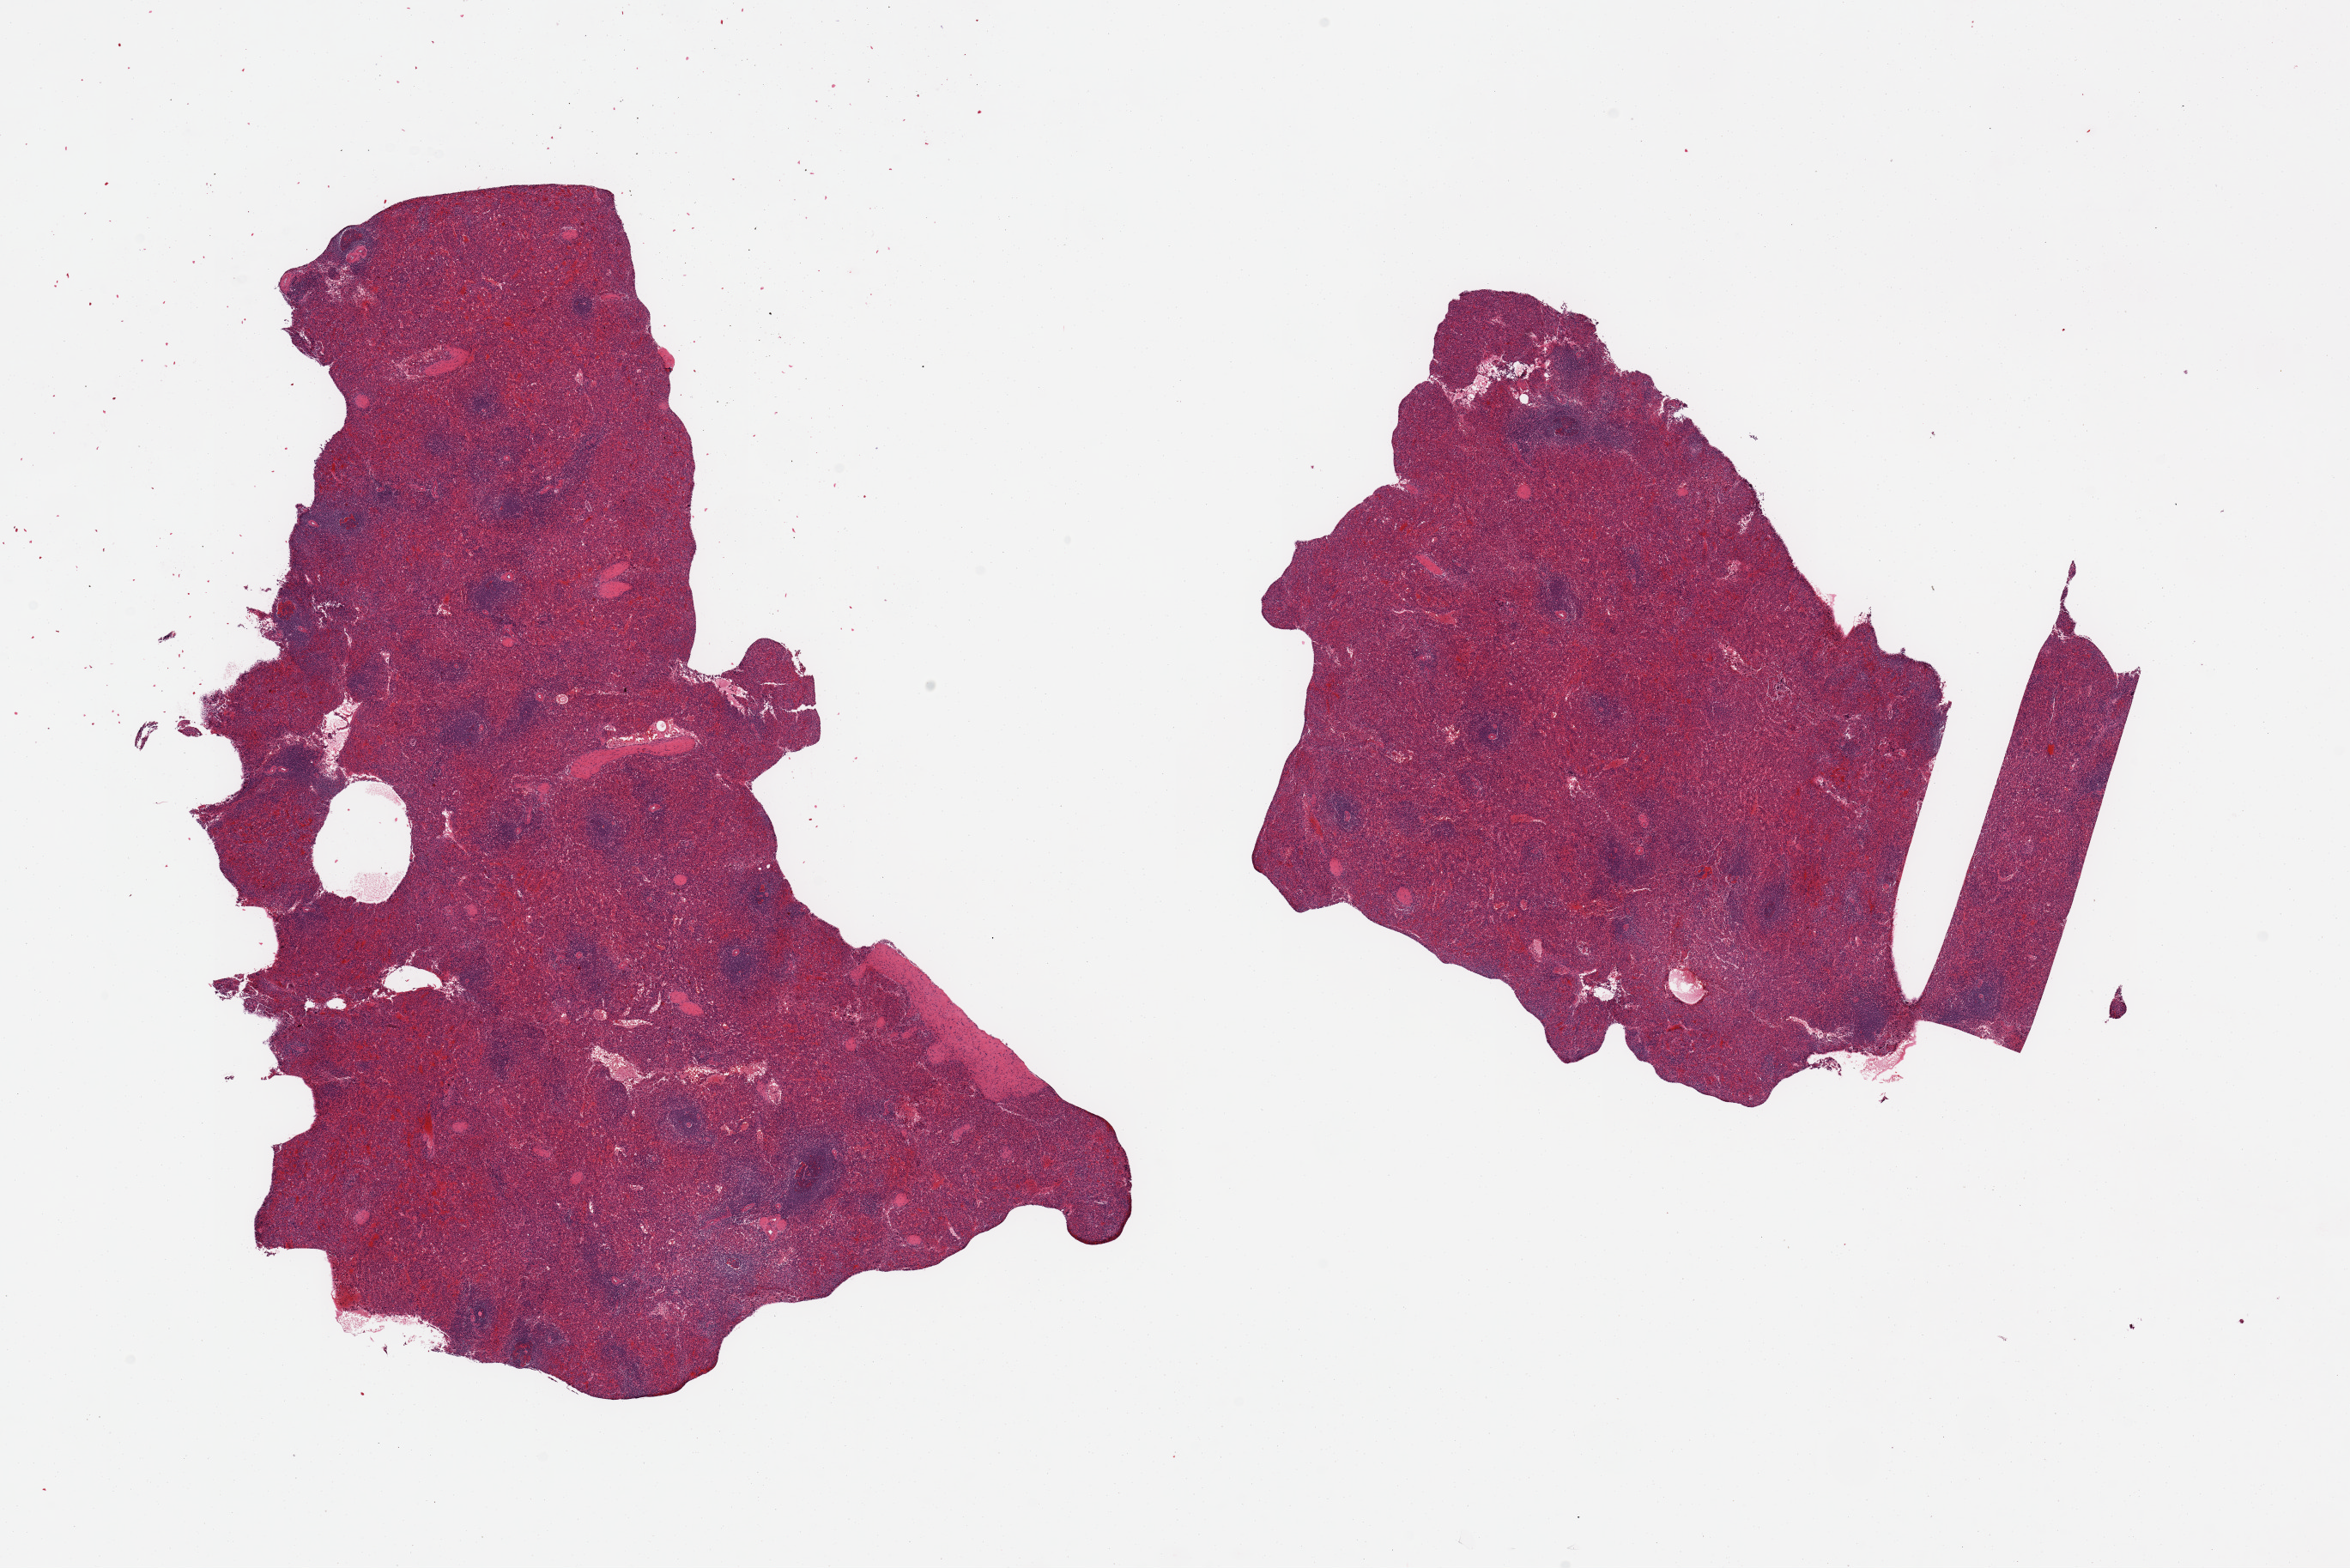
Whole-slide image, haematoxylin and eosin stain, brightfield, shown as a low-resolution overview of the whole scanned area (about 21.7 x 14.5 mm); PAXgene-fixed paraffin-embedded (PFPE) section; sampled site (target tissue): spleen; tissue donor sample. Donor sex: male.
Reviewer comment on this tissue sample: 2 pieces; moderate congestion.